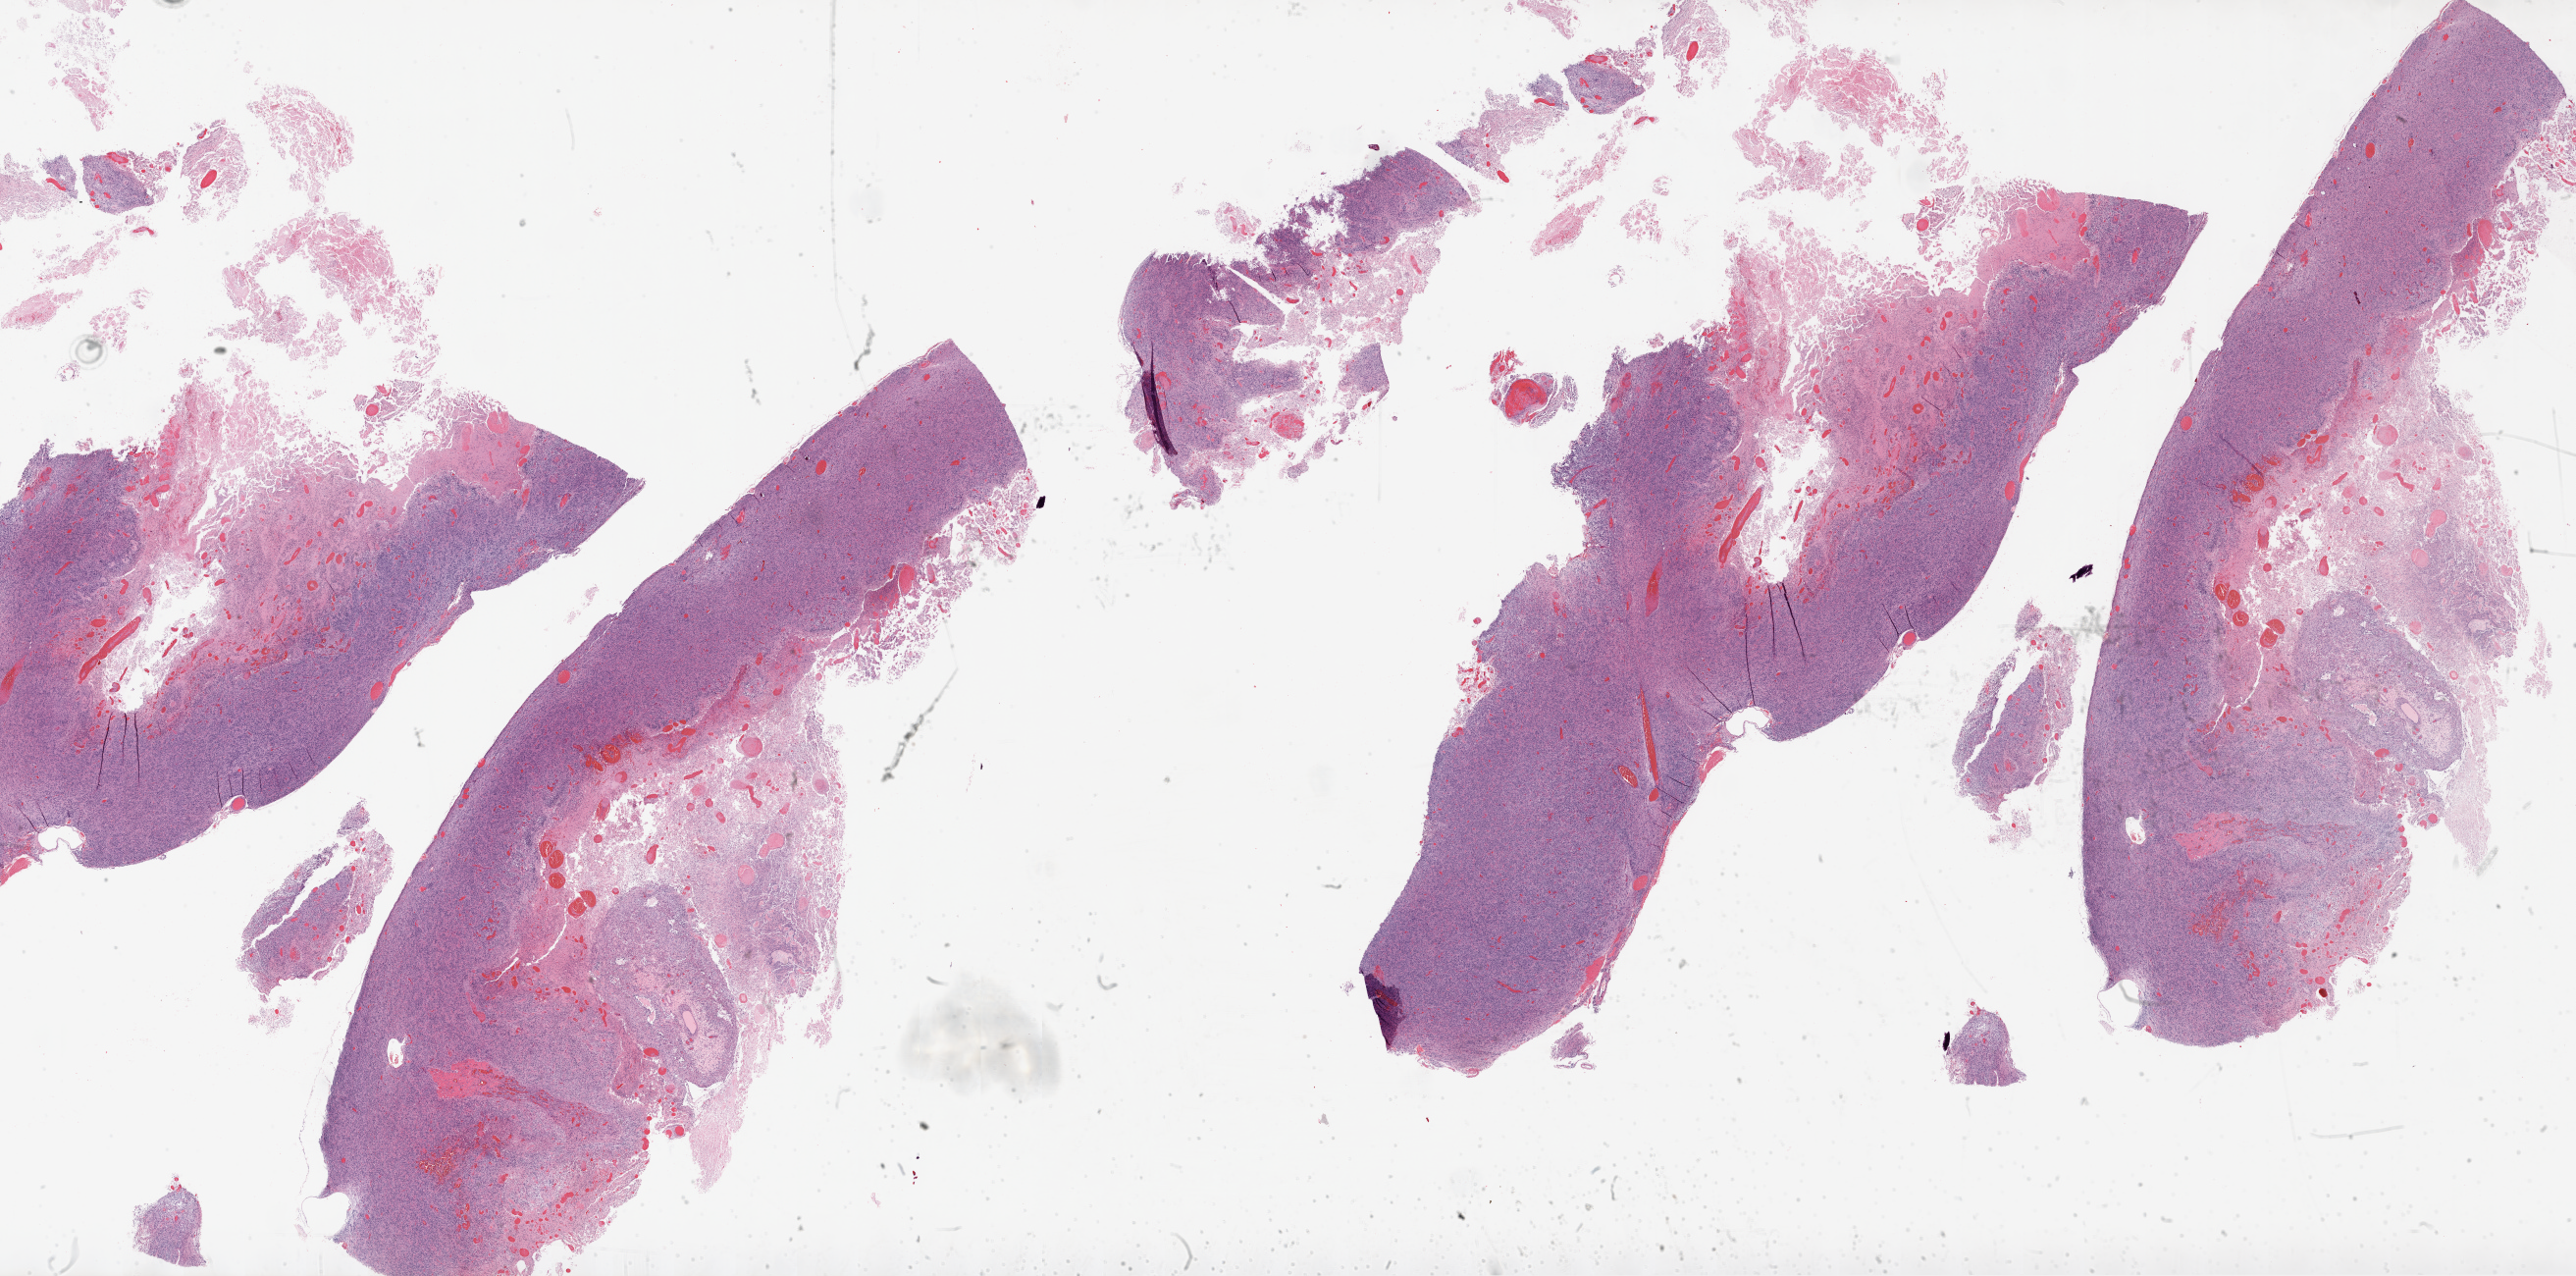
Whole-slide histology image, Hematoxylin and eosin (H&E) stained — shown as a low-resolution overview of the whole scanned area (about 42.1 x 20.9 mm), formalin-fixed paraffin-embedded (FFPE) diagnostic section, brain, primary tumour sample. Male patient; age at initial diagnosis 39 years.
Histologic diagnosis: Glioblastoma.